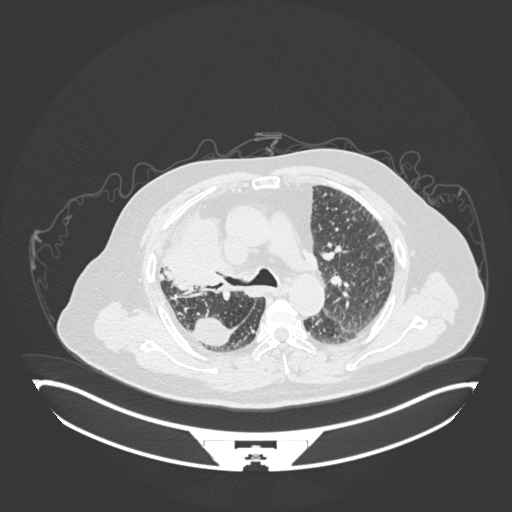
Chest CT, one axial slice; position 121 of 201 along the scan axis; 120 kVp; lung window (W 1500 / L -600 HU); 1 mm slice thickness; 512 × 512 image matrix, field of view 500 × 500 mm. Patient: male, 69 years. Case-level facts recorded for this patient, not image findings: clinical TNM (as recorded): T4 N3 M1.
Structures marked on this image (rectangle marked by the reading radiologist):
- lung tumour (recorded histology: adenocarcinoma): bounding box (x1, y1, x2, y2) in pixels: (162, 200, 233, 298)